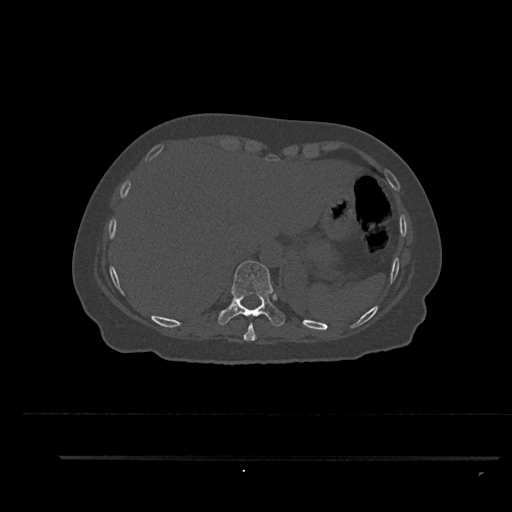
CT including the spine, one axial slice; position 372 of 797 along the scan axis; reconstruction kernel Br40s/3; 120 kVp; bone window (W 1800 / L 400 HU); 0.5 mm slice thickness; 512 × 512 image matrix, field of view 408 × 408 mm. Patient: female, 44 years. Case-level facts recorded for this patient, not image findings: primary cancer: renal; vertebrae with lytic lesions (as recorded): L1.
Structures marked on this image (semi-automatically segmented with operator editing):
- T10 vertebra: bounding box [x1, y1, x2, y2] px = [218, 260, 285, 331]
- T9 vertebra: [243, 323, 257, 341]